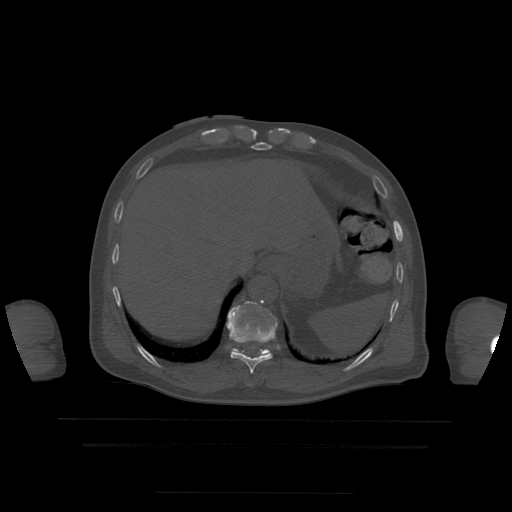
CT including the spine, one axial slice; slice 235 of 522 in the series (ordered by position); bone window (W 1800 / L 400 HU); 1.25 mm slice thickness; 512 × 512 image matrix. Patient age 68 years. From the clinical record (not read from this slice): primary cancer: urothelial.
Annotated regions visible in this slice (semi-automatic segmentation, software-assisted and operator-edited):
- T10 vertebra: bounding box (x1, y1, x2, y2) in pixels: (227, 302, 277, 374)
- T11 vertebra: (233, 302, 270, 357)